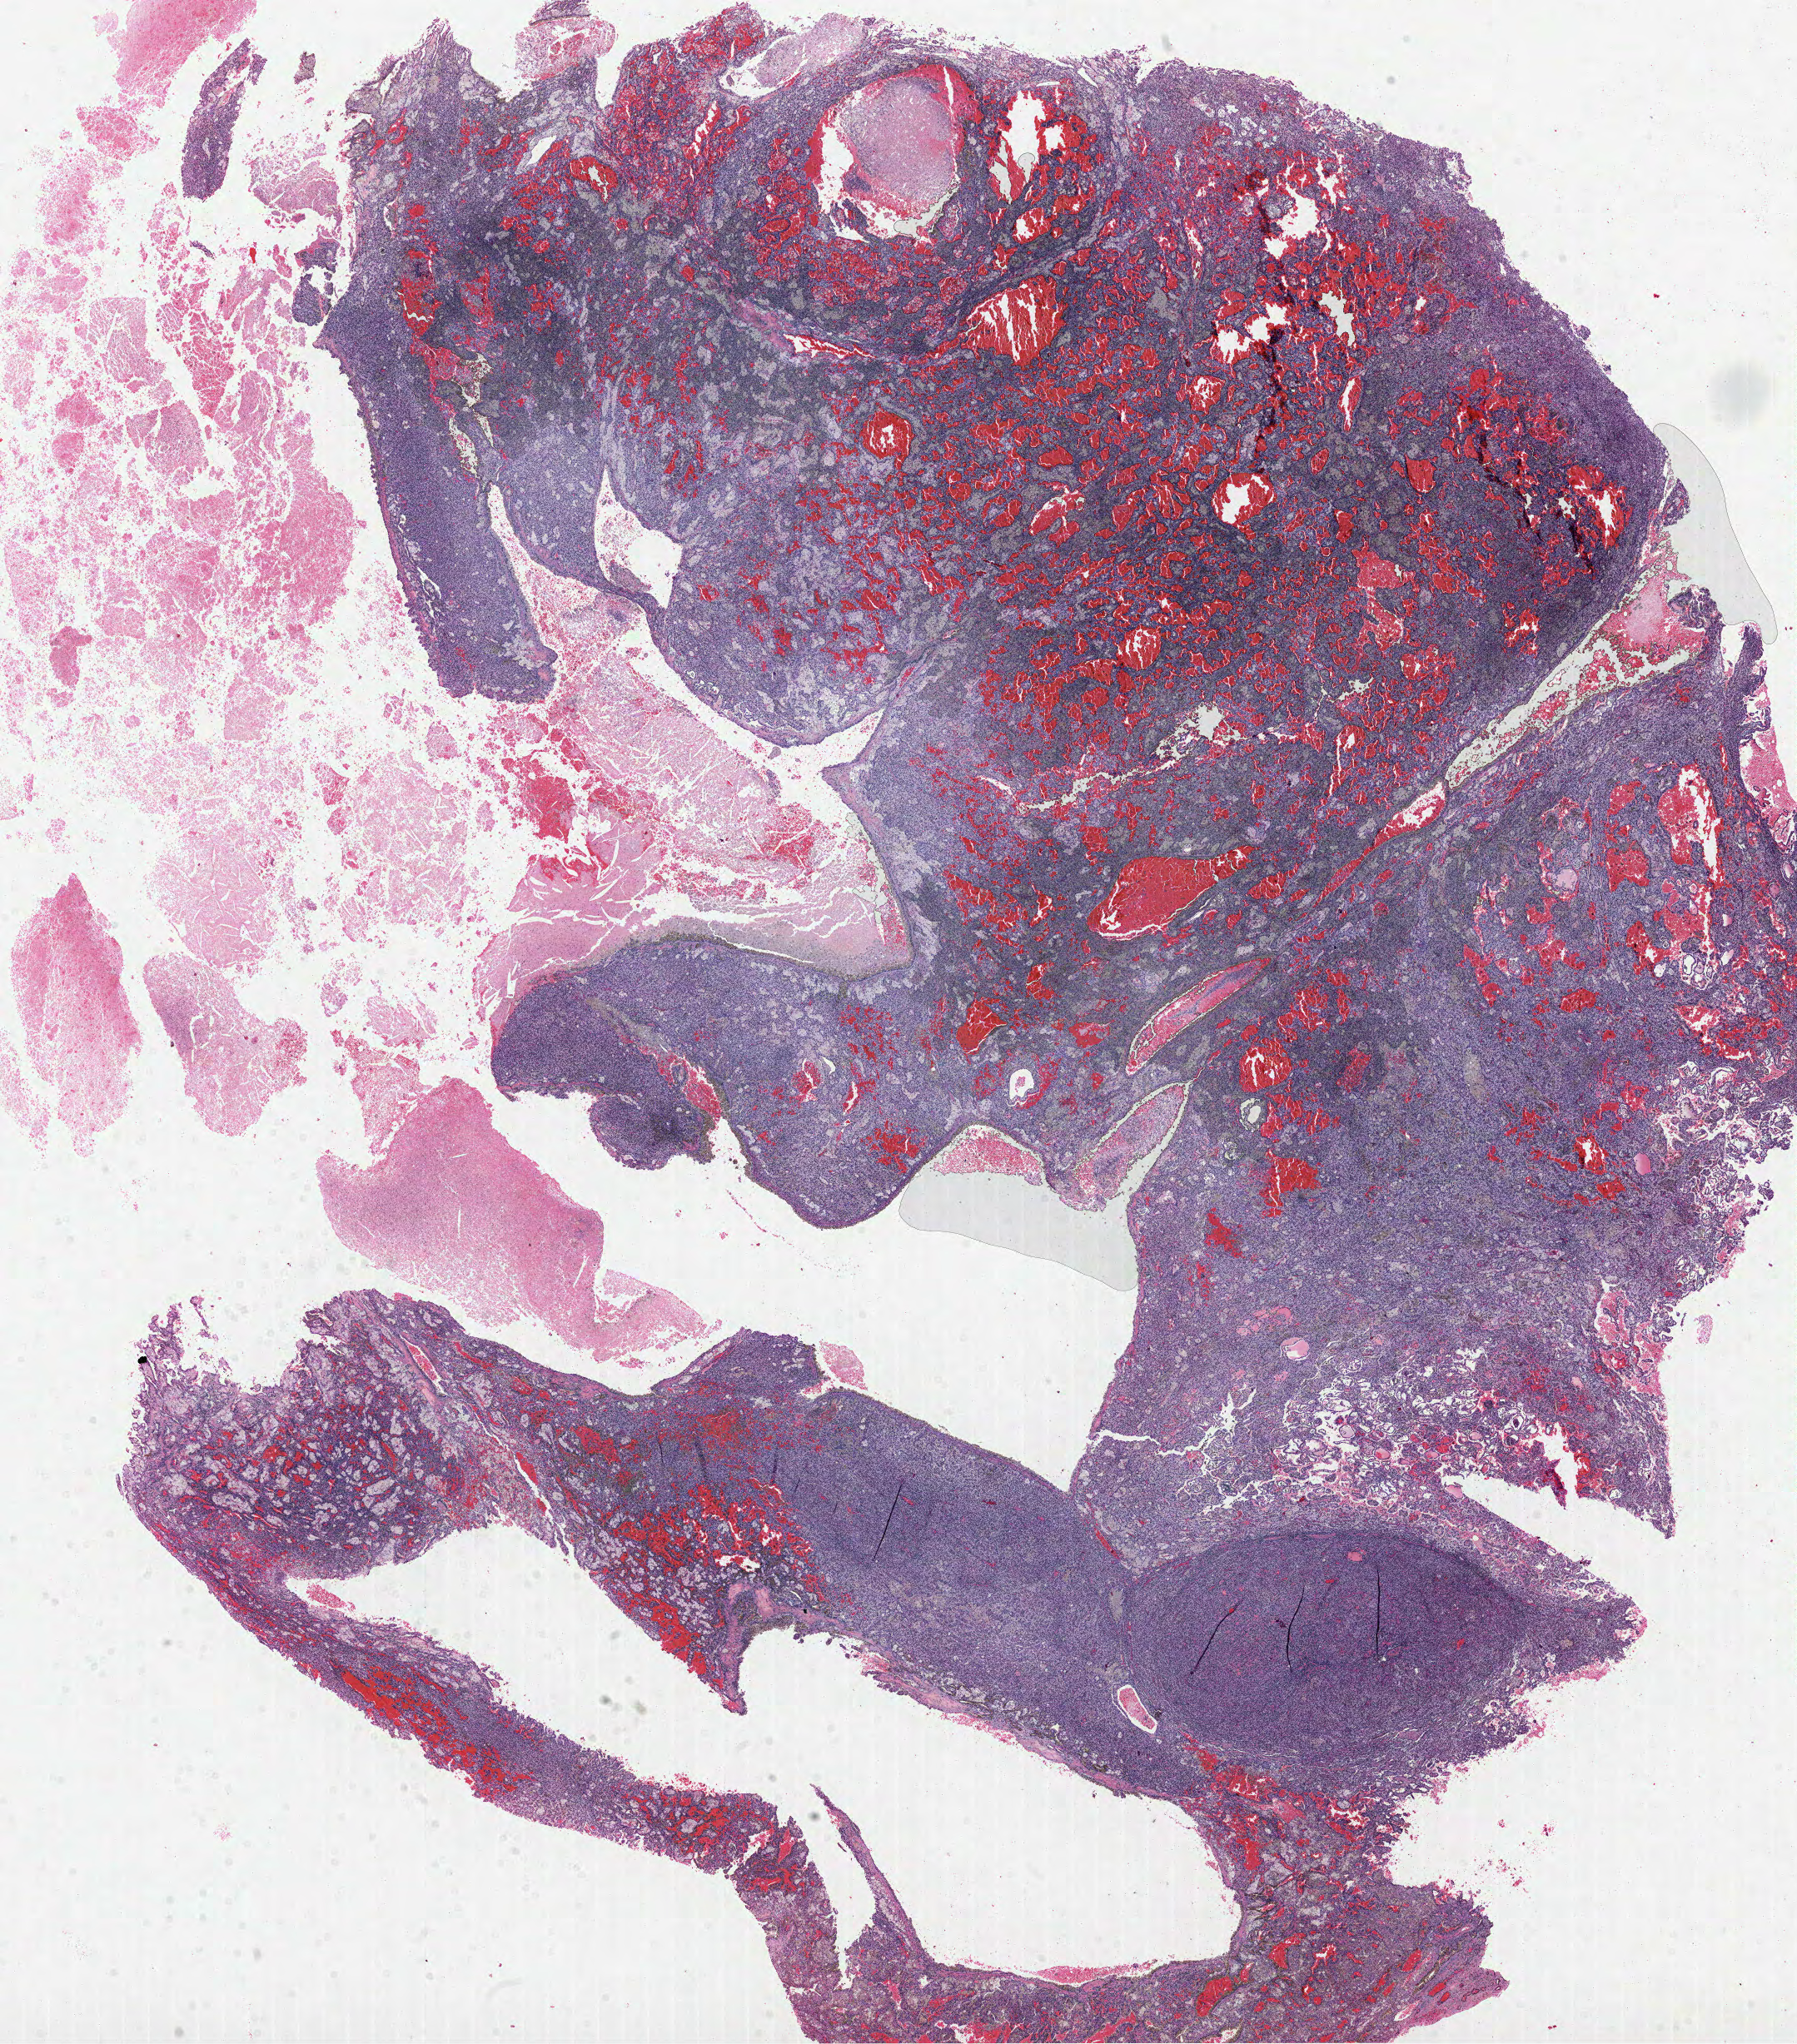
Whole-slide histology image, H&E-stained — whole scanned area (about 17.4 x 19.8 mm) shown as a low-resolution overview; formalin-fixed paraffin-embedded (FFPE) diagnostic section; kidney, primary tumour sample. Male patient; age at initial diagnosis 53 years.
AJCC pathologic stage: I. TNM: T1a NX. Laterality: right. Diagnosis: Papillary adenocarcinoma, NOS.